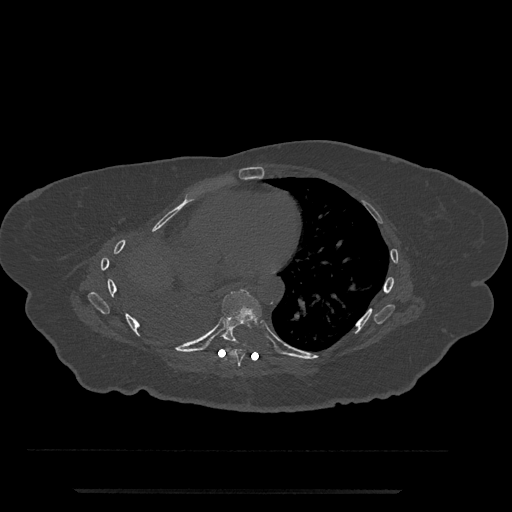
CT including the spine, one axial slice. Position 414 of 797 along the scan axis. Reconstruction kernel Br40s/3. Bone window (W 1800 / L 400 HU). 512 × 512 image matrix, field of view 440 × 440 mm. Female patient, age 51 years. Case-level facts recorded for this patient, not image findings: primary cancer: neuro; vertebrae with lytic lesions (as recorded): T8.
Annotated regions visible in this slice (semi-automatically segmented with operator editing):
- T7 vertebra: bounding box [x1, y1, x2, y2] px = [224, 347, 245, 367]
- T8 vertebra: [221, 289, 262, 342]